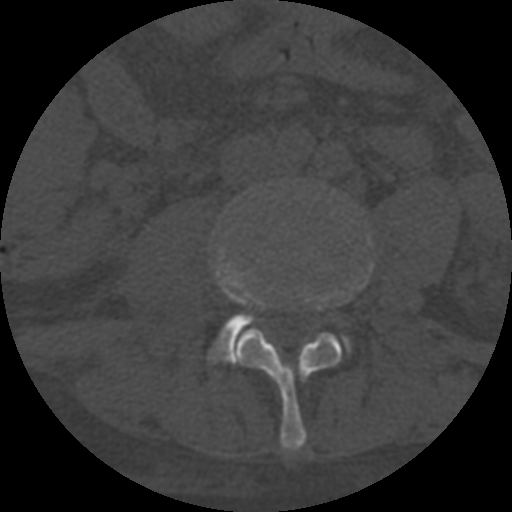
CT including the spine, one axial slice. Position 223 of 708 along the scan axis. 120 kVp. One of 3 acquisitions stored at this slice position. Bone window (W 1800 / L 400 HU). 1.25 mm slice thickness. 512 × 512 image matrix, field of view 160 × 160 mm. Patient age 55 years. Case-level facts recorded for this patient, not image findings: primary cancer: colon; vertebrae with lytic lesions (as recorded): T12, L1, L5.
Annotated regions visible in this slice (semi-automatically segmented with operator editing):
- L3 vertebra: bounding box [x1, y1, x2, y2] px = [219, 266, 371, 451]
- L4 vertebra: [211, 249, 371, 363]